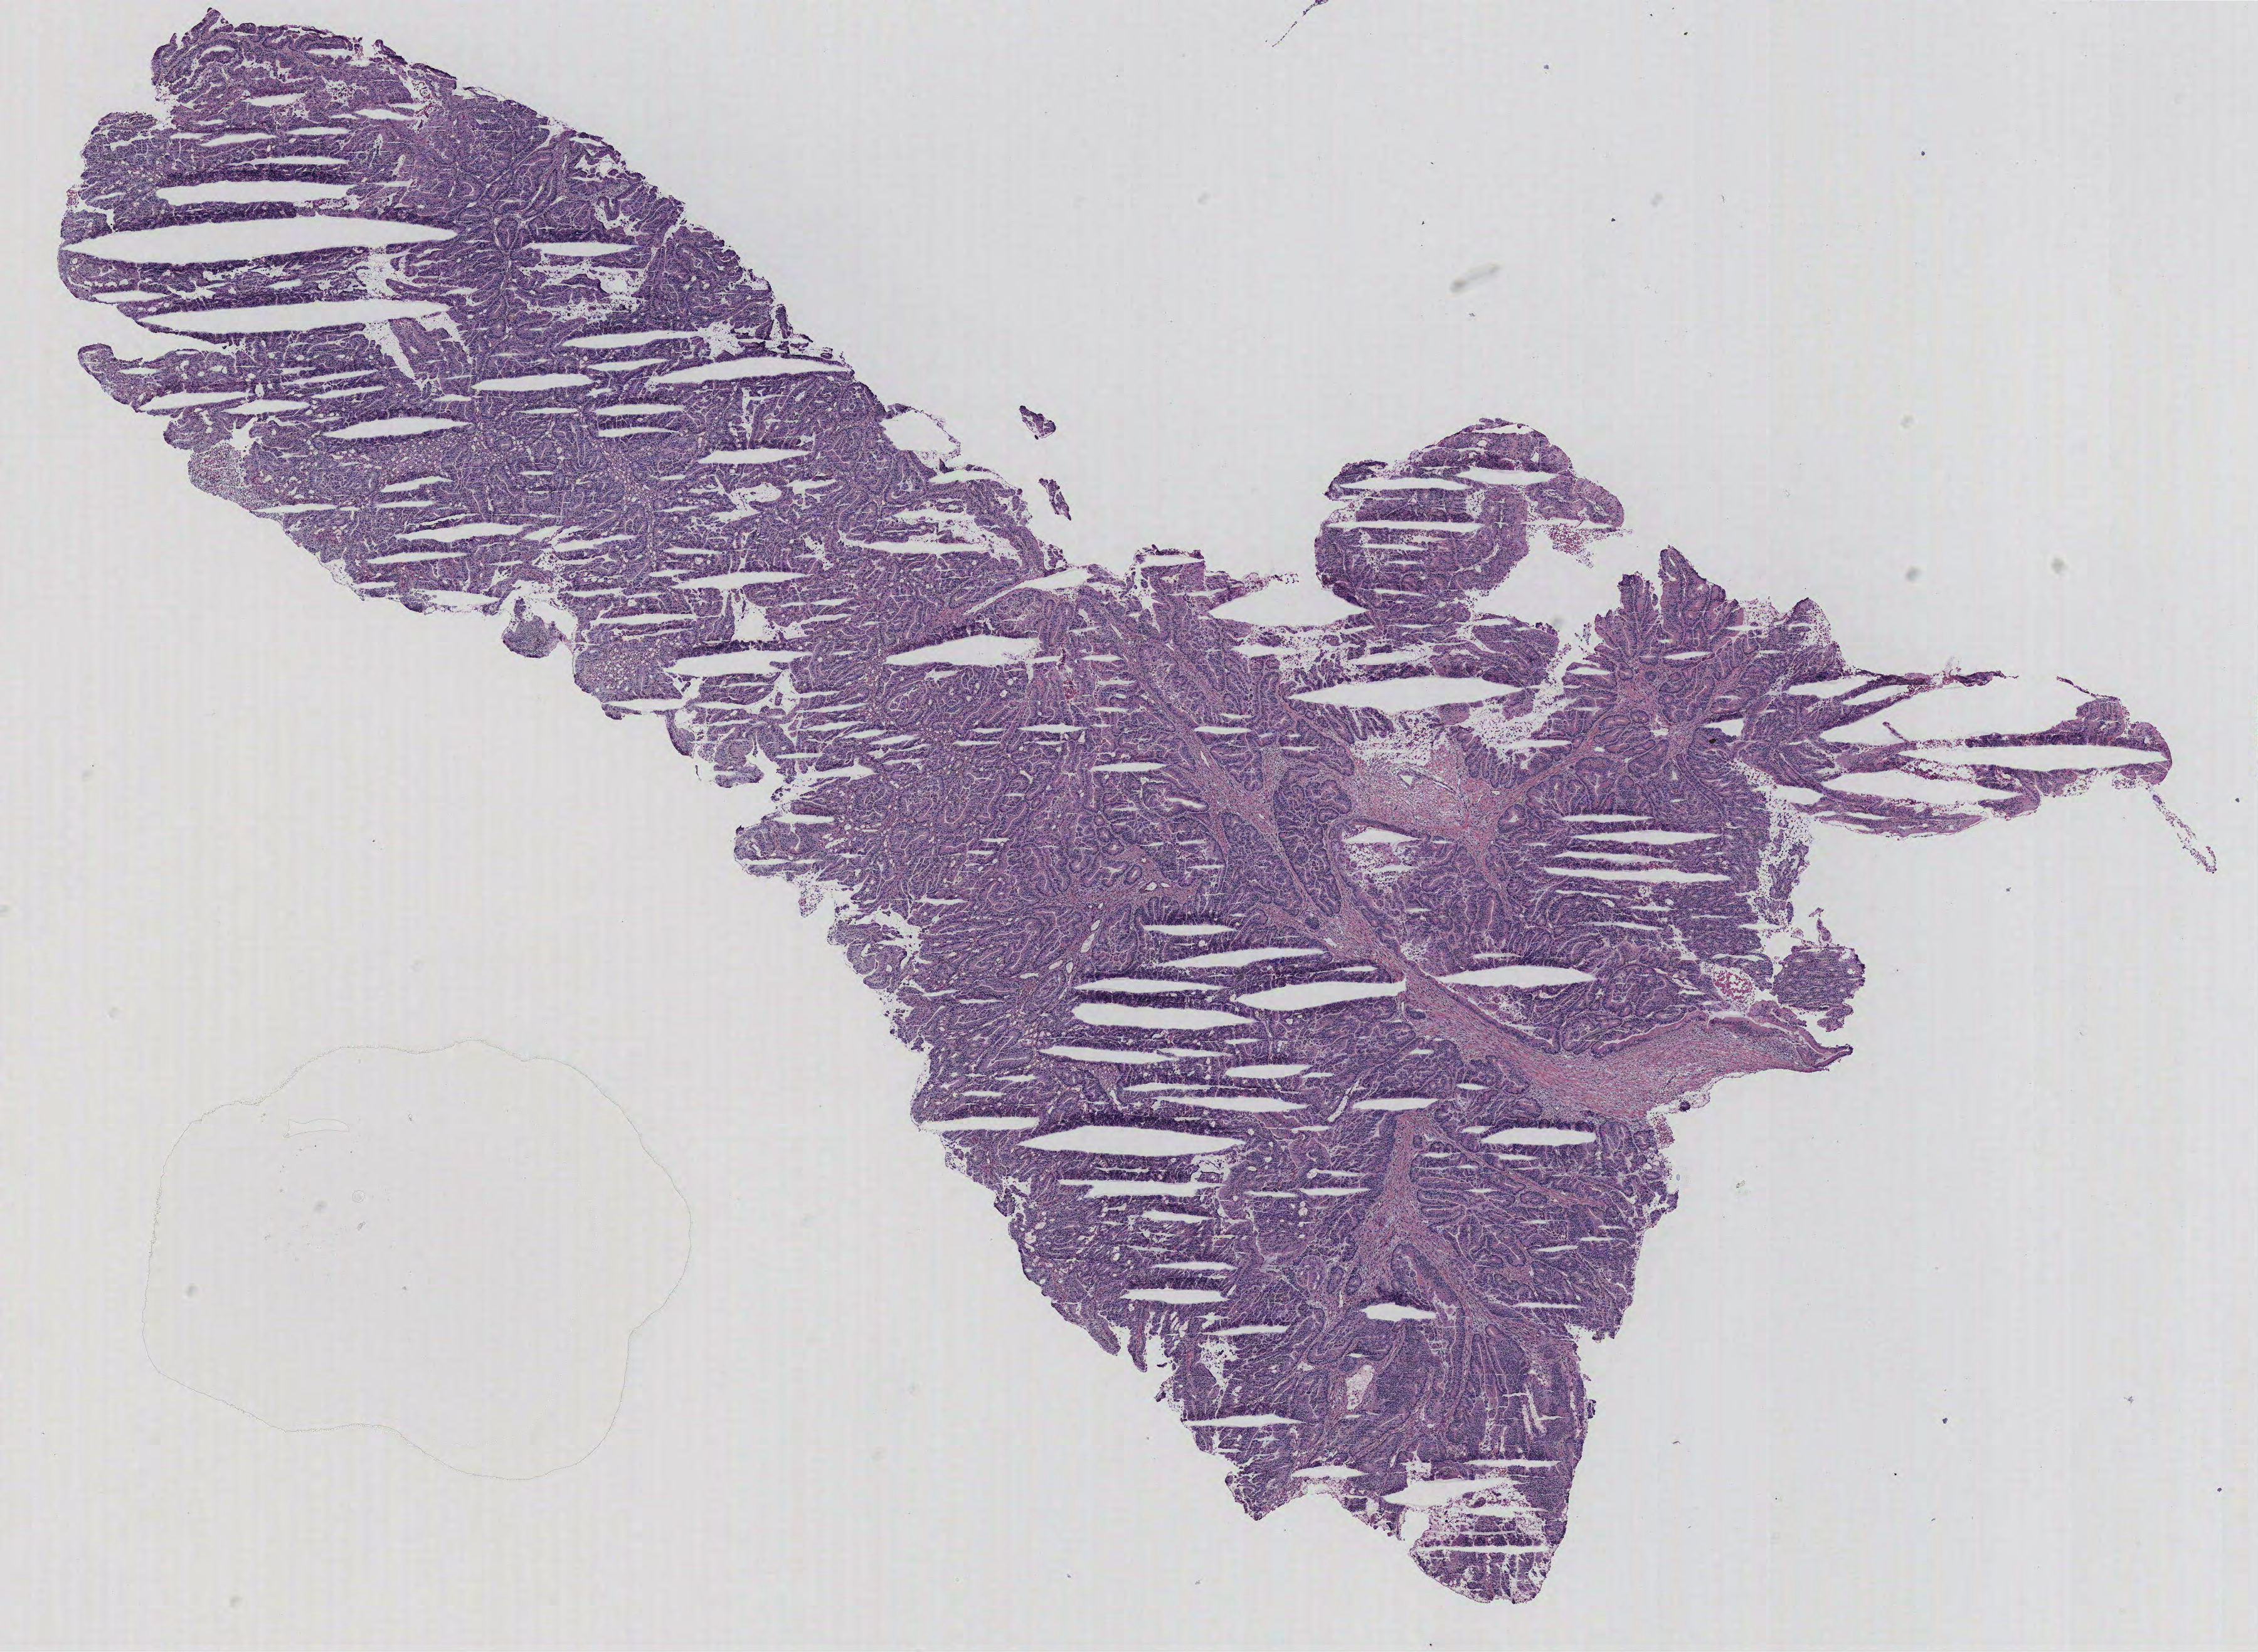
Whole-slide histology image, H&E-stained — low-resolution overview of the scanned area, about 14.4 x 10.5 mm, colon, tissue type not recorded. Patient sex: male.
* patient diagnosis: Adenocarcinoma, NOS